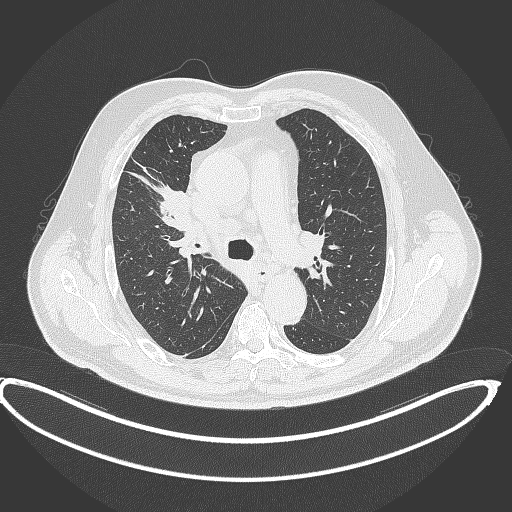
Chest CT, one axial slice; slice 272 of 390 in the series (ordered by position); reconstruction kernel B70f; lung window (W 1500 / L -600 HU); 1 mm slice thickness; 512 × 512 image matrix. Patient: male, 62 years. From the clinical record (not read from this slice): clinical TNM (as recorded): T1c N3 M1c.
Structures marked on this image (rectangle marked by the reading radiologist):
- lung tumour (recorded histology: adenocarcinoma): bounding box (x1, y1, x2, y2) in pixels: (152, 183, 195, 232)